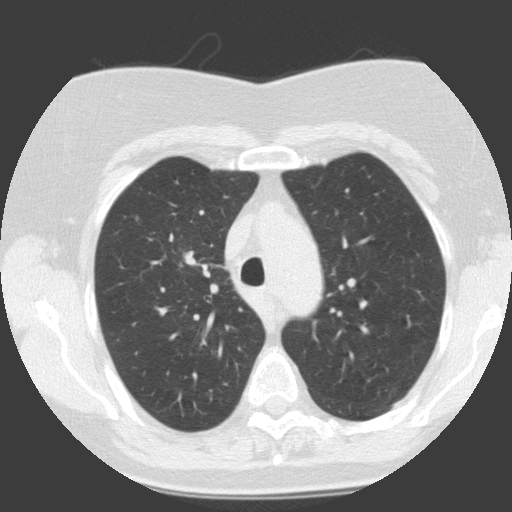
Low-dose screening chest CT, one axial slice; slice 104 of 146 in the series (ordered by position); lung window (W 1500 / L -600 HU); 512 × 512 image matrix, field of view 300 × 300 mm.
Annotated regions visible in this slice (outlined manually by an expert reader):
- lesion 1 (tumor, upper lobe of right lung): bounding box <183,251,194,263> (left, top, right, bottom; pixels)